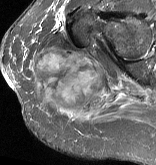
MRI of an extremity soft-tissue mass, one axial slice; slice 37 of 57 in the series (ordered by position); STIR; MR volume resampled by the dataset authors to the PET/CT grid (not the native acquisition matrix); 3.27 mm slice thickness; 156 × 165 image matrix. Female patient. From the clinical record (not read from this slice): histological type: epithelioid sarcoma with vascular differentiation; site of the primary tumour: right buttock.
Annotated regions visible in this slice (expert contour drawn on MRI and transferred to this co-registered scan by the dataset authors):
- gross tumour volume (mass): bounding box (x1, y1, x2, y2) in pixels: (29, 50, 112, 113)